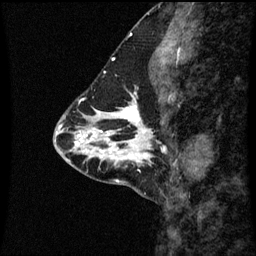
Breast MRI (dynamic contrast-enhanced), one sagittal slice. Slice 24 of 60 in the series (ordered by position). Dynamic contrast-enhanced series, image 2 of 3 at this slice position (ordered by acquisition). 1.5 T. TE 4.2 ms, TR 8.9 ms. 256 × 256 image matrix, field of view 200 × 200 mm. Female patient, age 43 years. Case-level facts recorded for this patient, not image findings: setting: breast cancer imaged before/during neoadjuvant chemotherapy; receptor status: HR-positive, HER2-negative.
Structures marked on this image (semi-automatic segmentation, software-assisted and operator-edited):
- analysis volume of interest (the breast-tissue region the enhancement analysis was run in; not a lesion): bounding box <110,100,171,163> (left, top, right, bottom; pixels)
- tumour enhancement mask (voxels above the 70 % enhancement threshold inside the analysis volume of interest): <110,100,165,161>